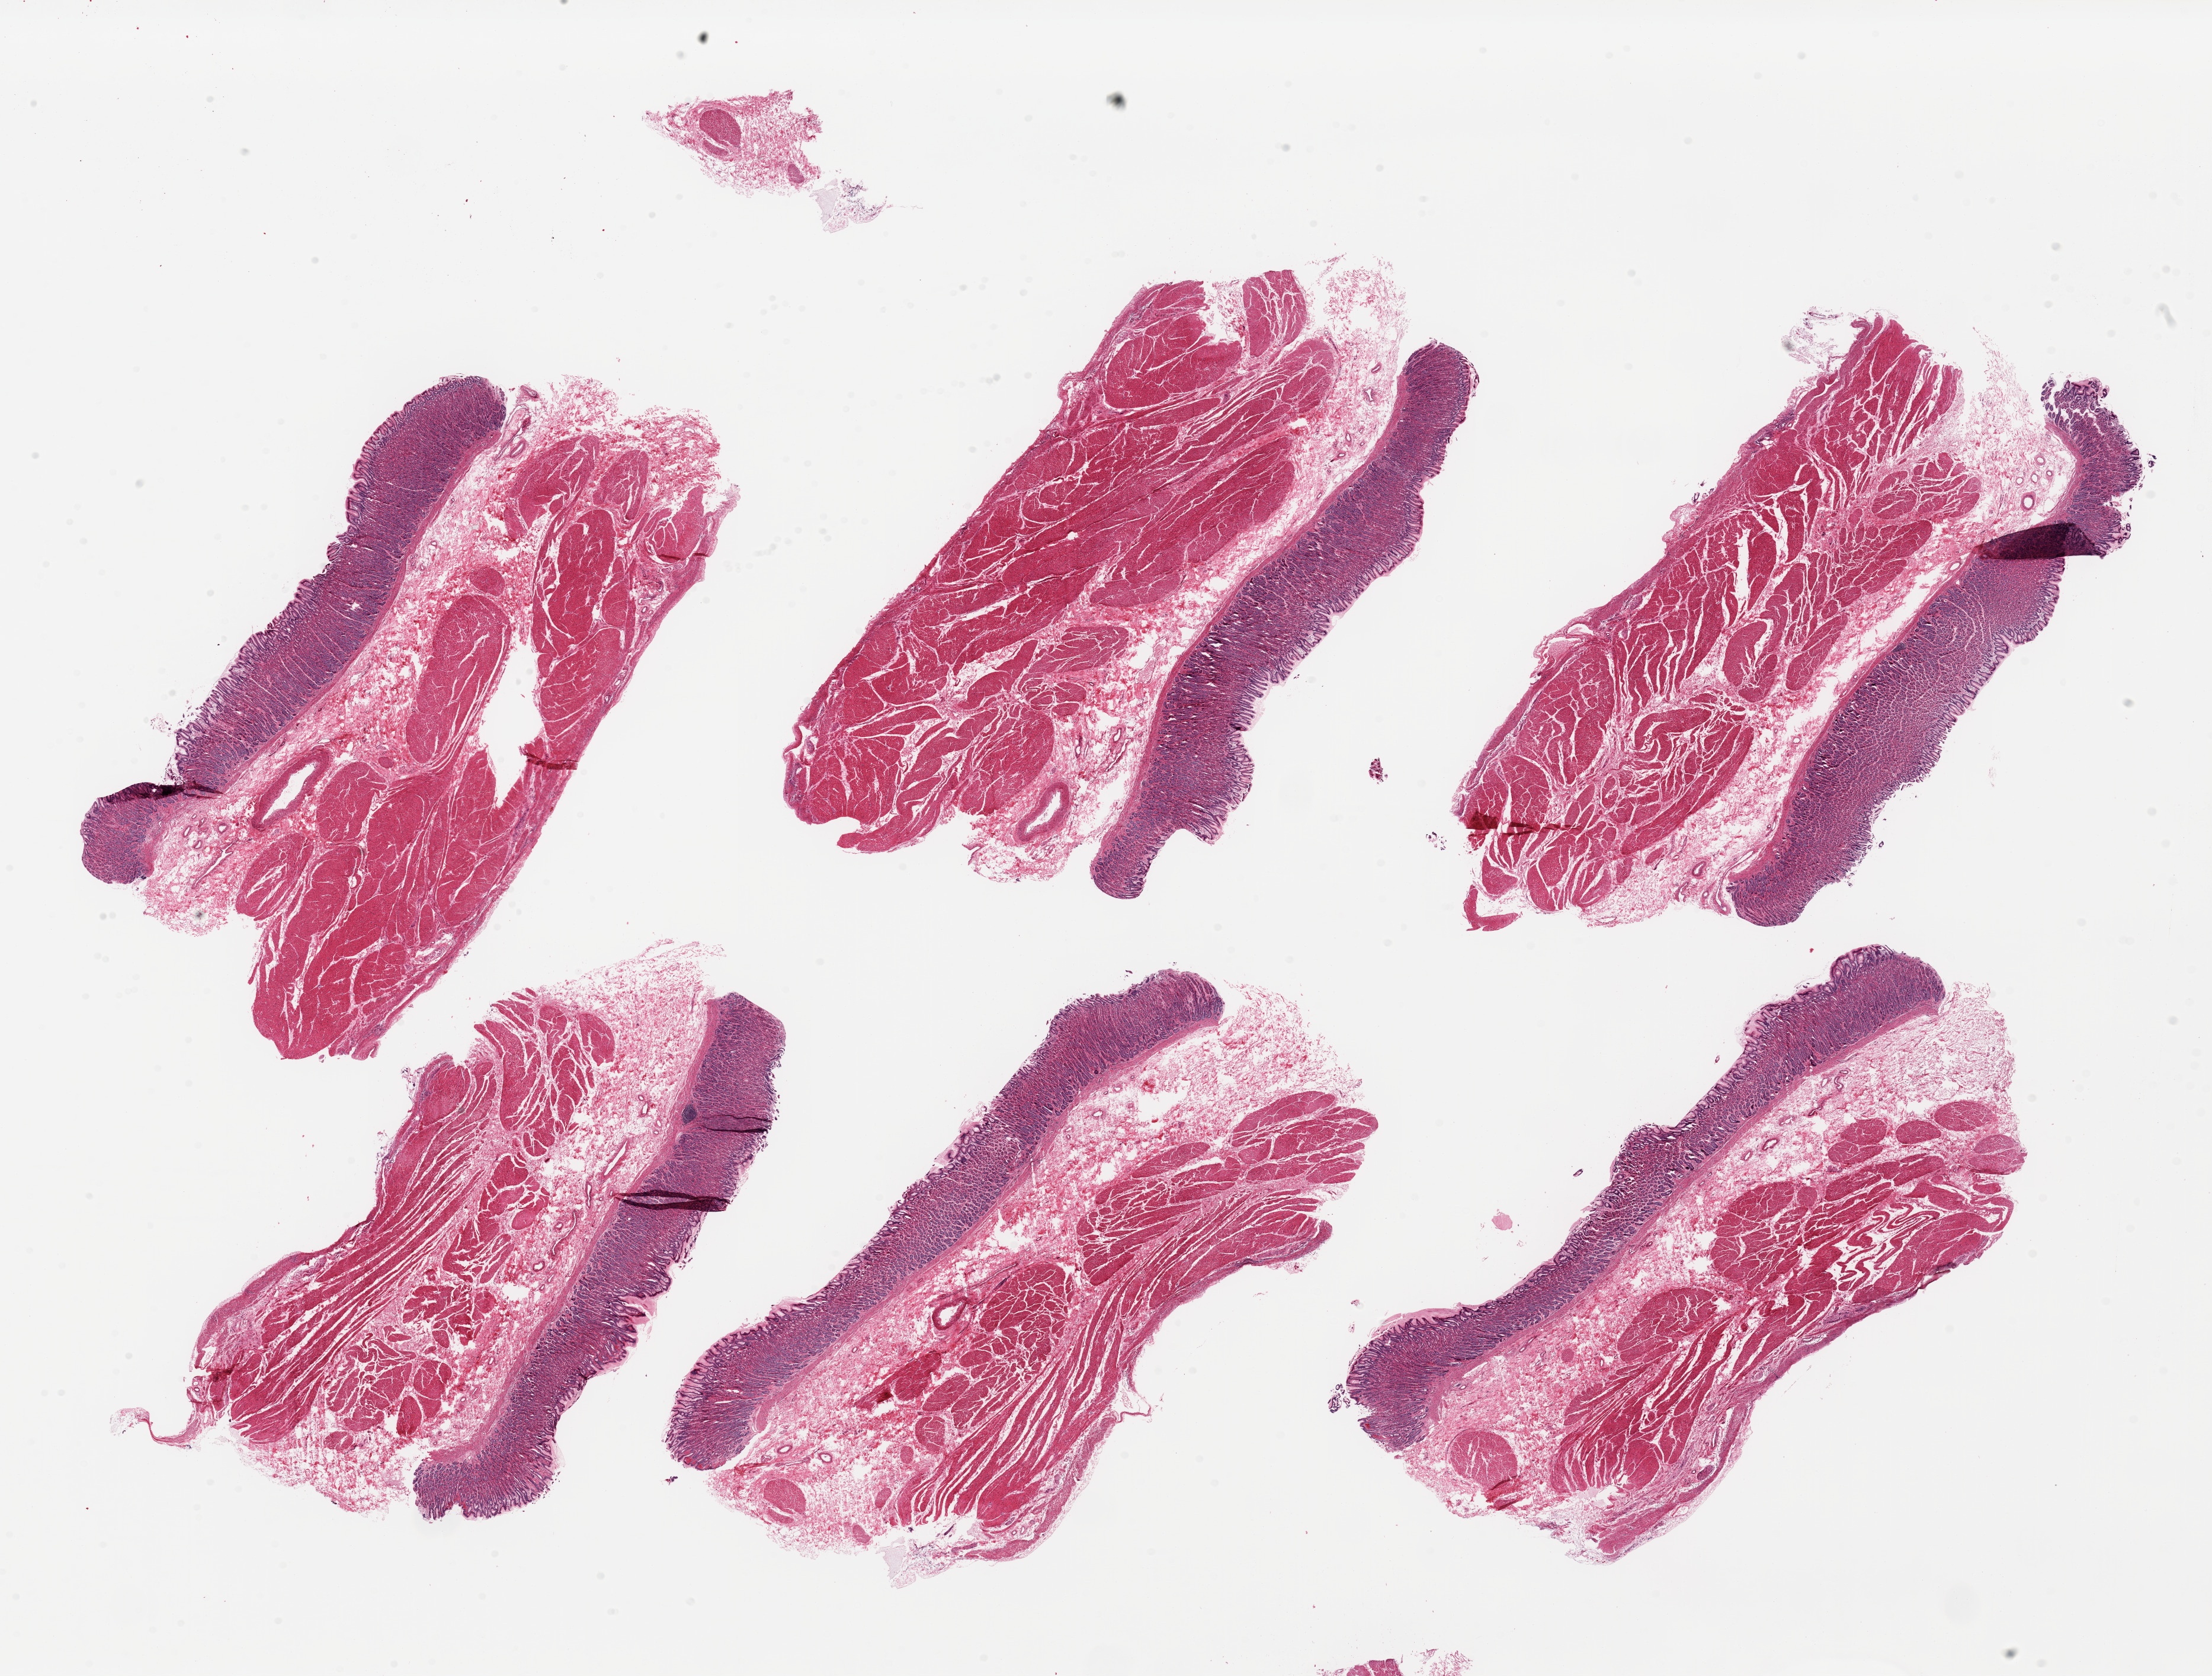
H&E whole-slide image, brightfield, low-resolution overview of the scanned area, about 29.5 x 22.4 mm (slide scanned at 20x); PAXgene-fixed, paraffin-embedded tissue; sampled site (target tissue): stomach; donor tissue sample. Donor sex: female.
Reviewer comment on this tissue sample: 6 pieces; full thickness sections, rare aggregate of lymphocytes.